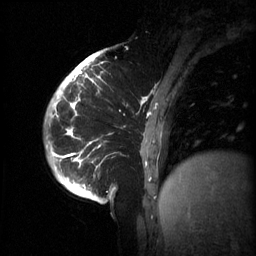
Breast MRI (dynamic contrast-enhanced), one sagittal slice; 3 images stored at this slice position (order not interpretable as contrast timing); 1.5 T; TE 4.2 ms, TR 11 ms; 256 × 256 image matrix, field of view 220 × 220 mm. Patient: female, 51 years.
Structures marked on this image (semi-automatically segmented with operator editing):
- analysis volume of interest (the breast-tissue region the enhancement analysis was run in; not a lesion): box from (x=63, y=80) to (x=186, y=201) px
- tumour enhancement mask (voxels above the 70 % enhancement threshold inside the analysis volume of interest): (x=63, y=80)–(x=169, y=185)